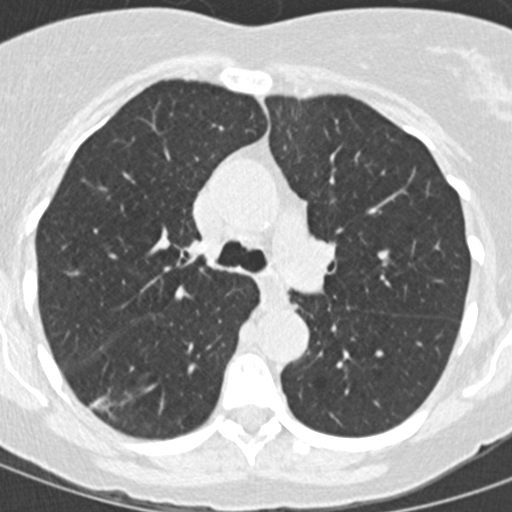
Low-dose screening chest CT, one axial slice; reconstruction kernel B30f; lung window (W 1500 / L -600 HU); 2 mm slice thickness; 512 × 512 image matrix, field of view 270 × 270 mm.
Structures marked on this image (manually delineated by an expert):
- lesion 1 (tumor, lower lobe of right lung): bounding box (x1, y1, x2, y2) in pixels: (90, 397, 110, 411)